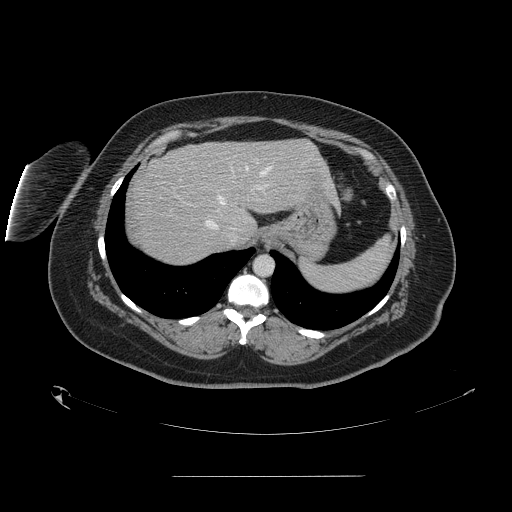
Contrast-enhanced abdominal CT, one axial slice; position 123 of 164 along the scan axis; intravenous contrast given; soft-tissue window (W 400 / L 40 HU); 512 × 512 image matrix, field of view 495 × 495 mm. Female patient, age 52 years. From the clinical record (not read from this slice): diagnosis: colorectal cancer liver metastases, imaged before liver resection; multiple liver metastases: yes; largest metastasis: 3.5 cm; disease in both lobes: no.
Annotated regions visible in this slice (manually delineated by an expert):
- hepatic veins: bounding box [x1, y1, x2, y2] px = [205, 166, 271, 242]
- liver: [127, 140, 335, 266]
- planned liver remnant (the part of the liver to remain after resection): [170, 140, 335, 224]
- portal vein (with intrahepatic branches): [179, 179, 261, 190]